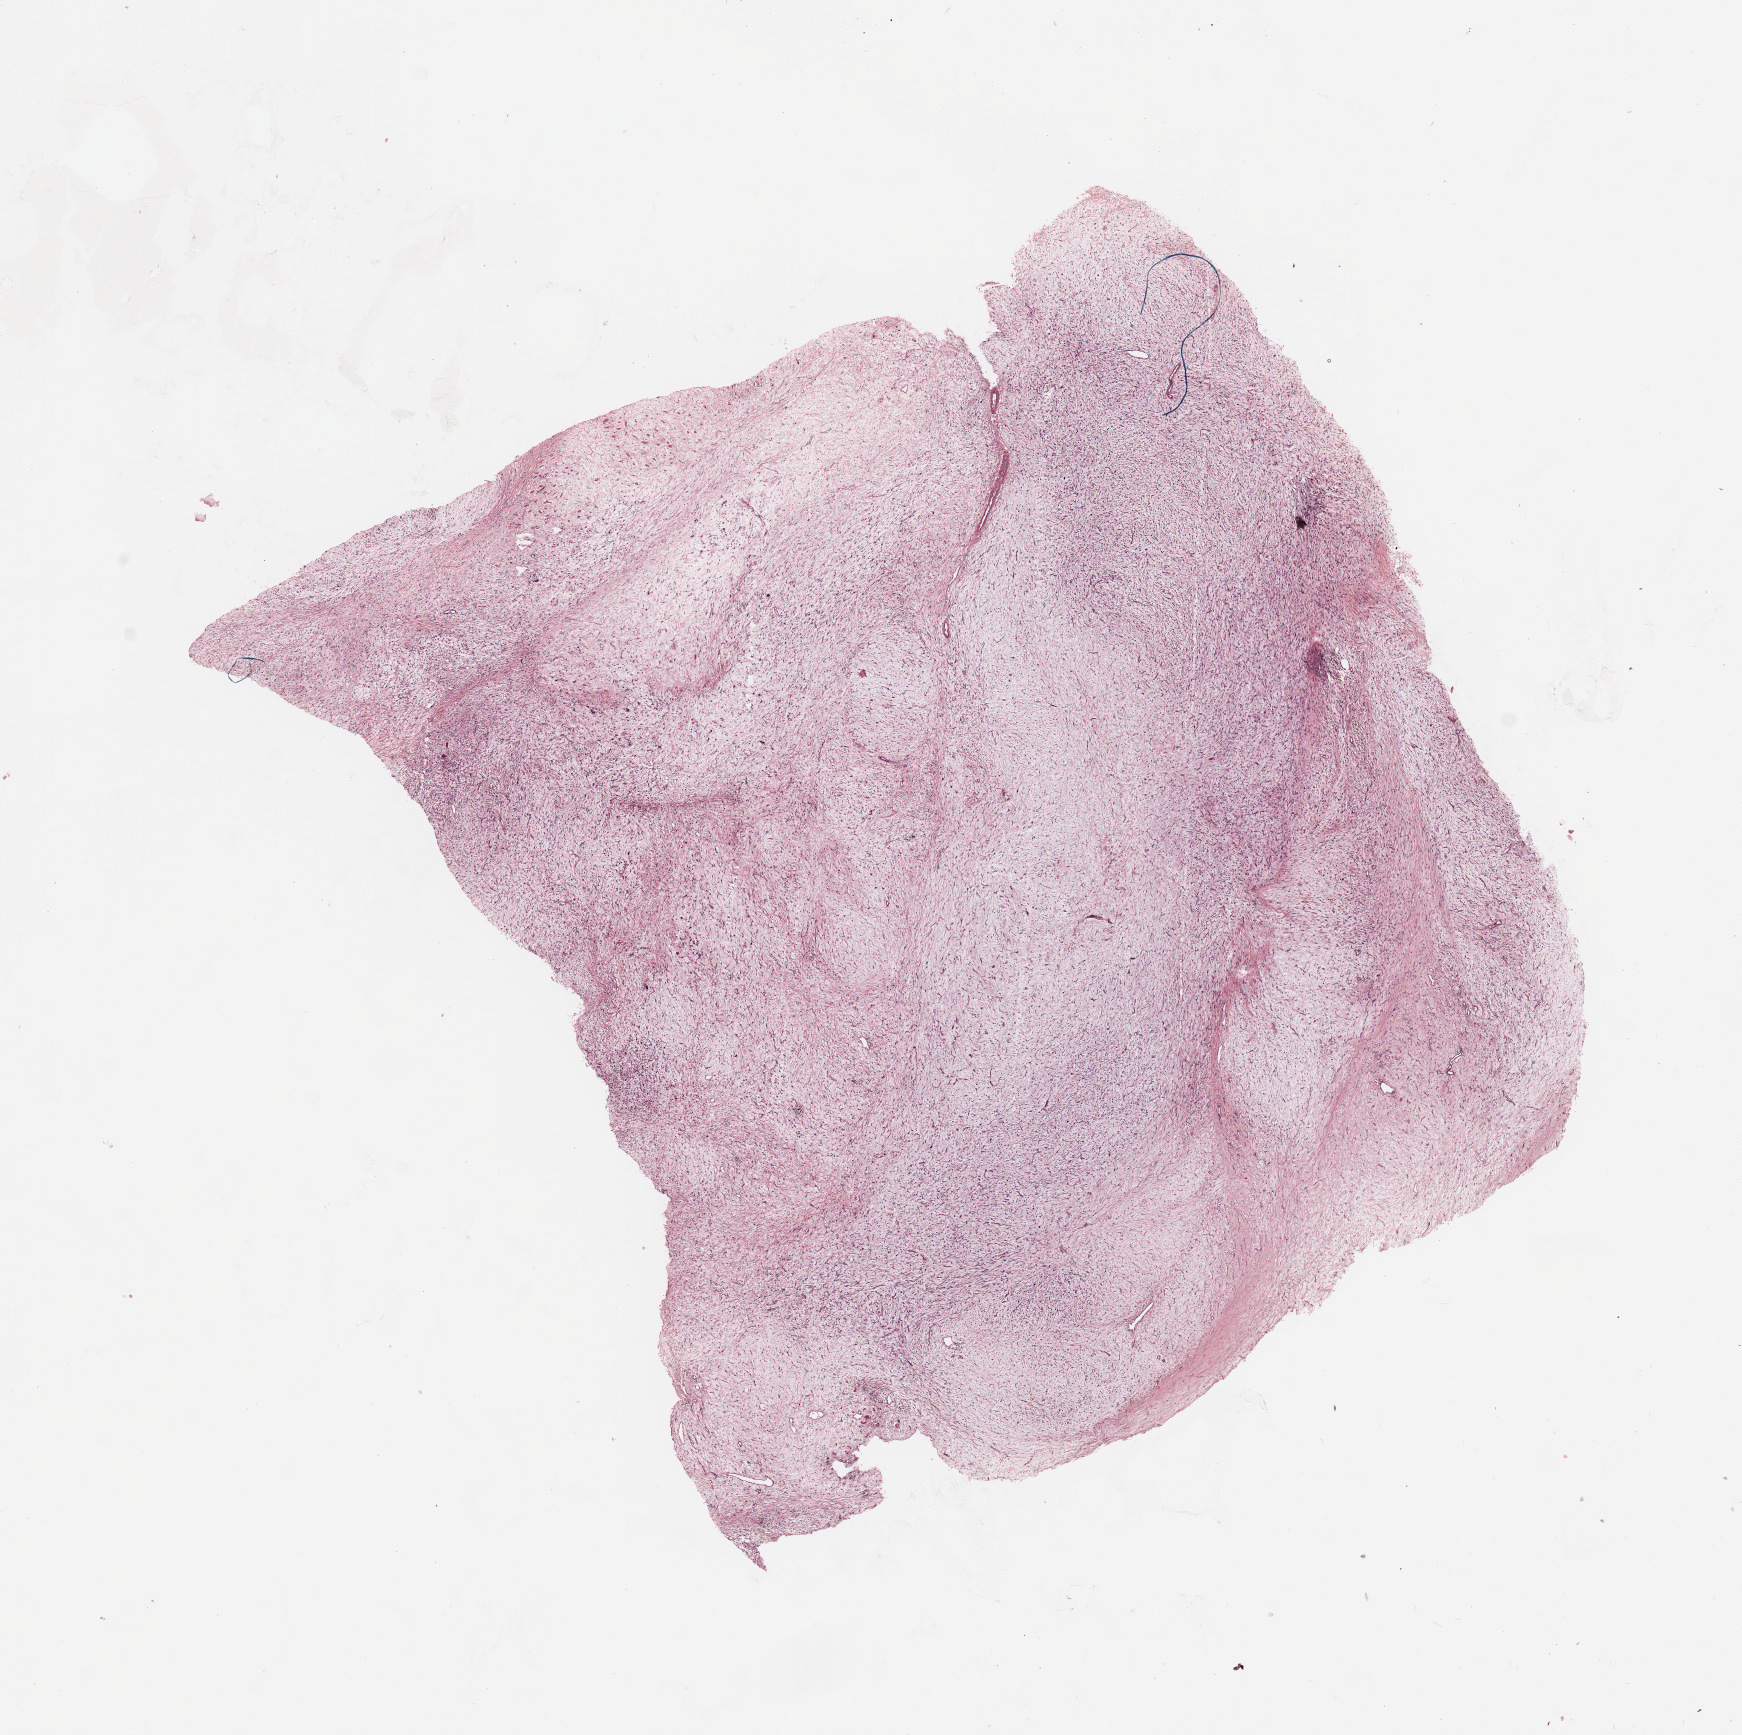
H&E whole-slide image — shown as a low-resolution overview of the whole scanned area (about 13.8 x 13.7 mm, from a 20x scan); tumour tissue sample. Patient: female, age 77 years.
Patient diagnosis (cohort enrolment): sarcoma (site not recorded at cohort level). Primary tumour site (as recorded): lower extremity.